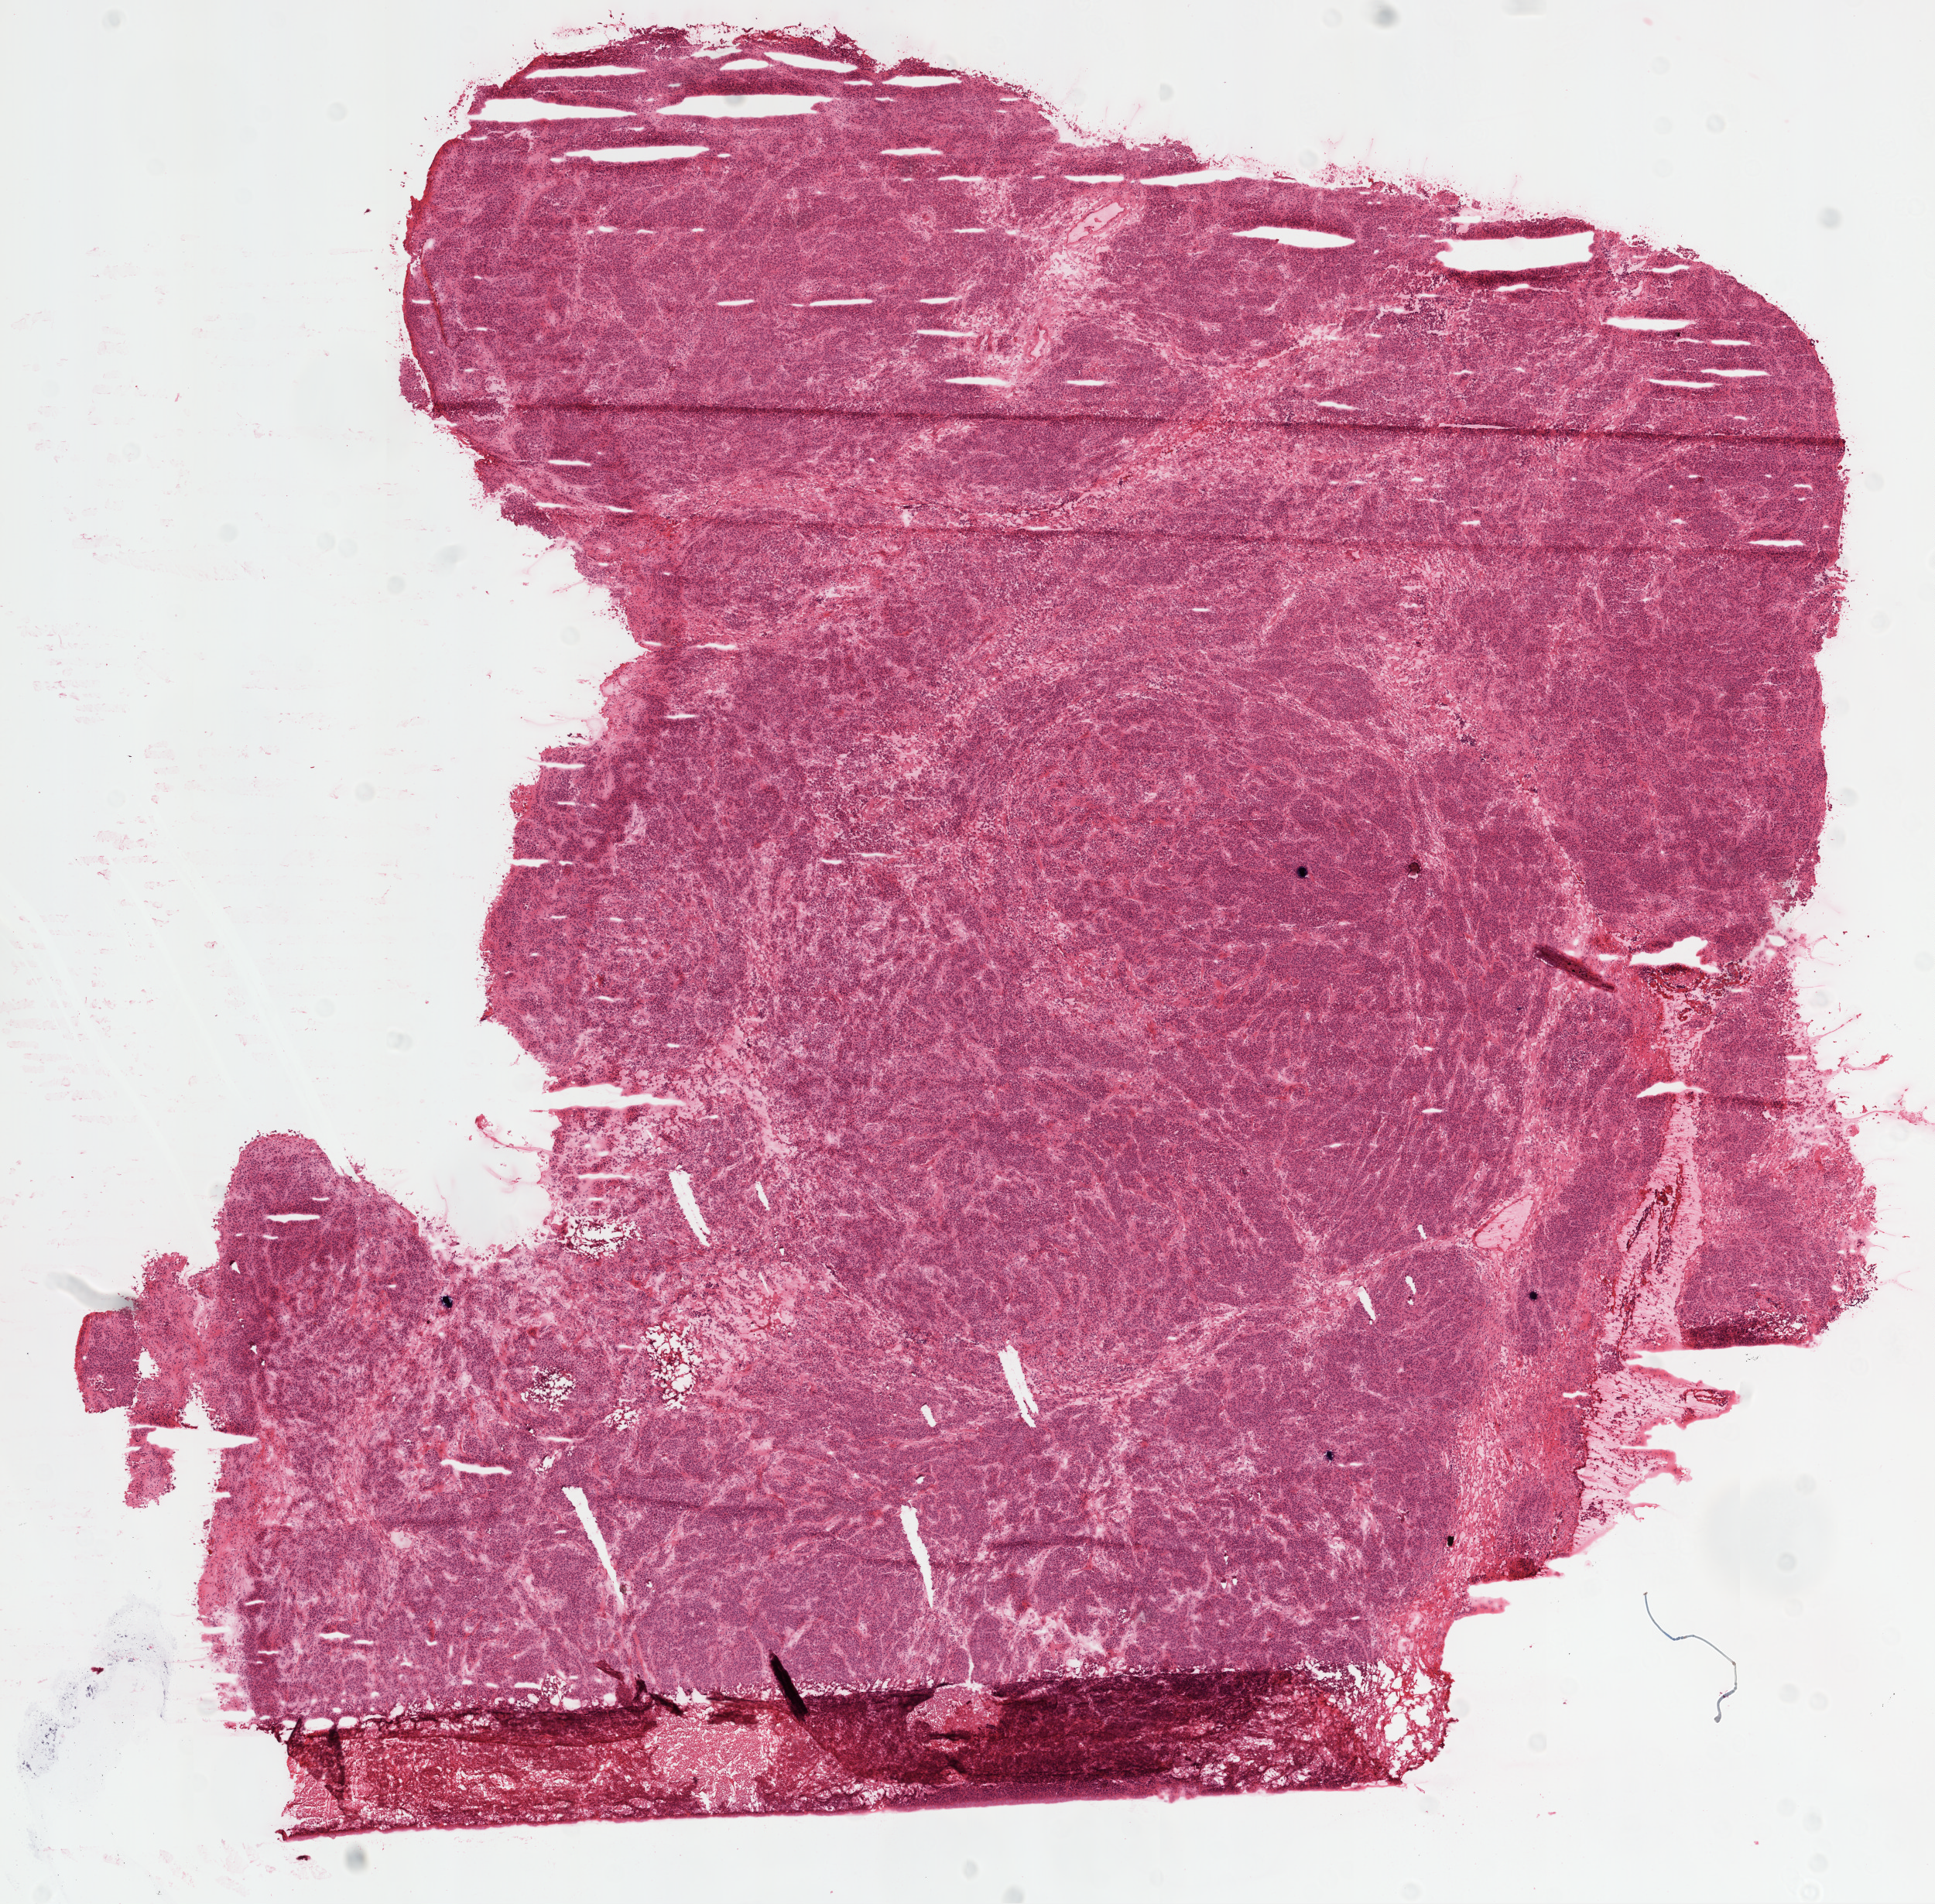
Whole-slide histology image, H&E — low-resolution overview of the scanned area, about 10.0 x 9.9 mm (acquisition: 20x scan), frozen section, ovary, primary tumour sample. Patient: female, age at initial diagnosis 74 years. Histologic grade: G3 (poorly differentiated). Slide review estimates, as recorded: tumour cells 95%, tumour nuclei 80%, normal cells 0%, stromal cells 0%, necrosis 5%. Infiltration values recorded for this section: lymphocyte infiltration 10%.
- laterality: right
- histologic diagnosis: Serous cystadenocarcinoma, NOS
- FIGO stage: IC